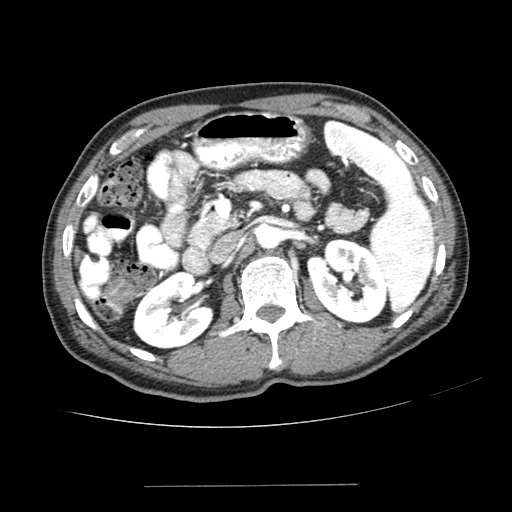
Contrast-enhanced abdominal CT (liver protocol), one axial slice. Slice 133 of 187 in the series (ordered by position). Reconstruction kernel SOFT. 100 kVp. One of 2 acquisitions stored at this slice position. Soft-tissue window (W 400 / L 40 HU). 2.5 mm slice thickness. 512 × 512 image matrix, field of view 360 × 360 mm. From the clinical record (not read from this slice): diagnosis: hepatocellular carcinoma (patient treated with transarterial chemoembolisation; whether this scan precedes or follows treatment is not stated here); TNM stage (as recorded): Stage-I.
Annotated regions visible in this slice (semi-automatic segmentation, software-assisted and operator-edited):
- liver parenchyma outside the tumour (the mass and vessels are separate outlines, so this box may not span the whole liver): bounding box <74,250,80,261> (left, top, right, bottom; pixels)